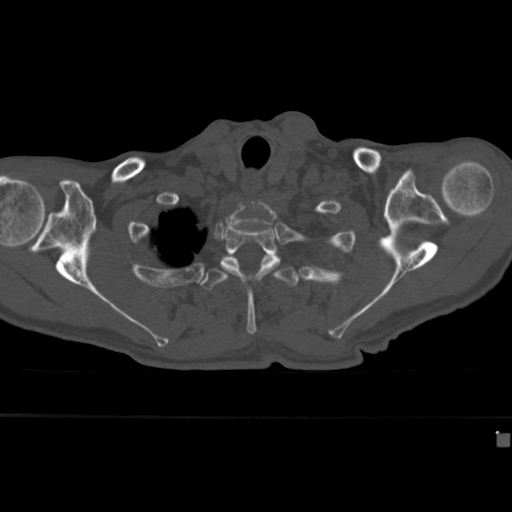
CT including the spine, one axial slice. Position 341 of 430 along the scan axis. Reconstruction kernel Br40s. Bone window (W 1800 / L 400 HU). 1.5 mm slice thickness. 512 × 512 image matrix, field of view 337 × 337 mm. Male patient, age 64 years. From the clinical record (not read from this slice): primary cancer: uterus; vertebrae with lytic lesions (as recorded): T1, T4, T5, T7, L5.
Structures marked on this image (semi-automatic segmentation, software-assisted and operator-edited):
- T2 vertebra: bounding box (x1, y1, x2, y2) in pixels: (220, 218, 281, 289)
- T3 vertebra: (199, 257, 299, 335)